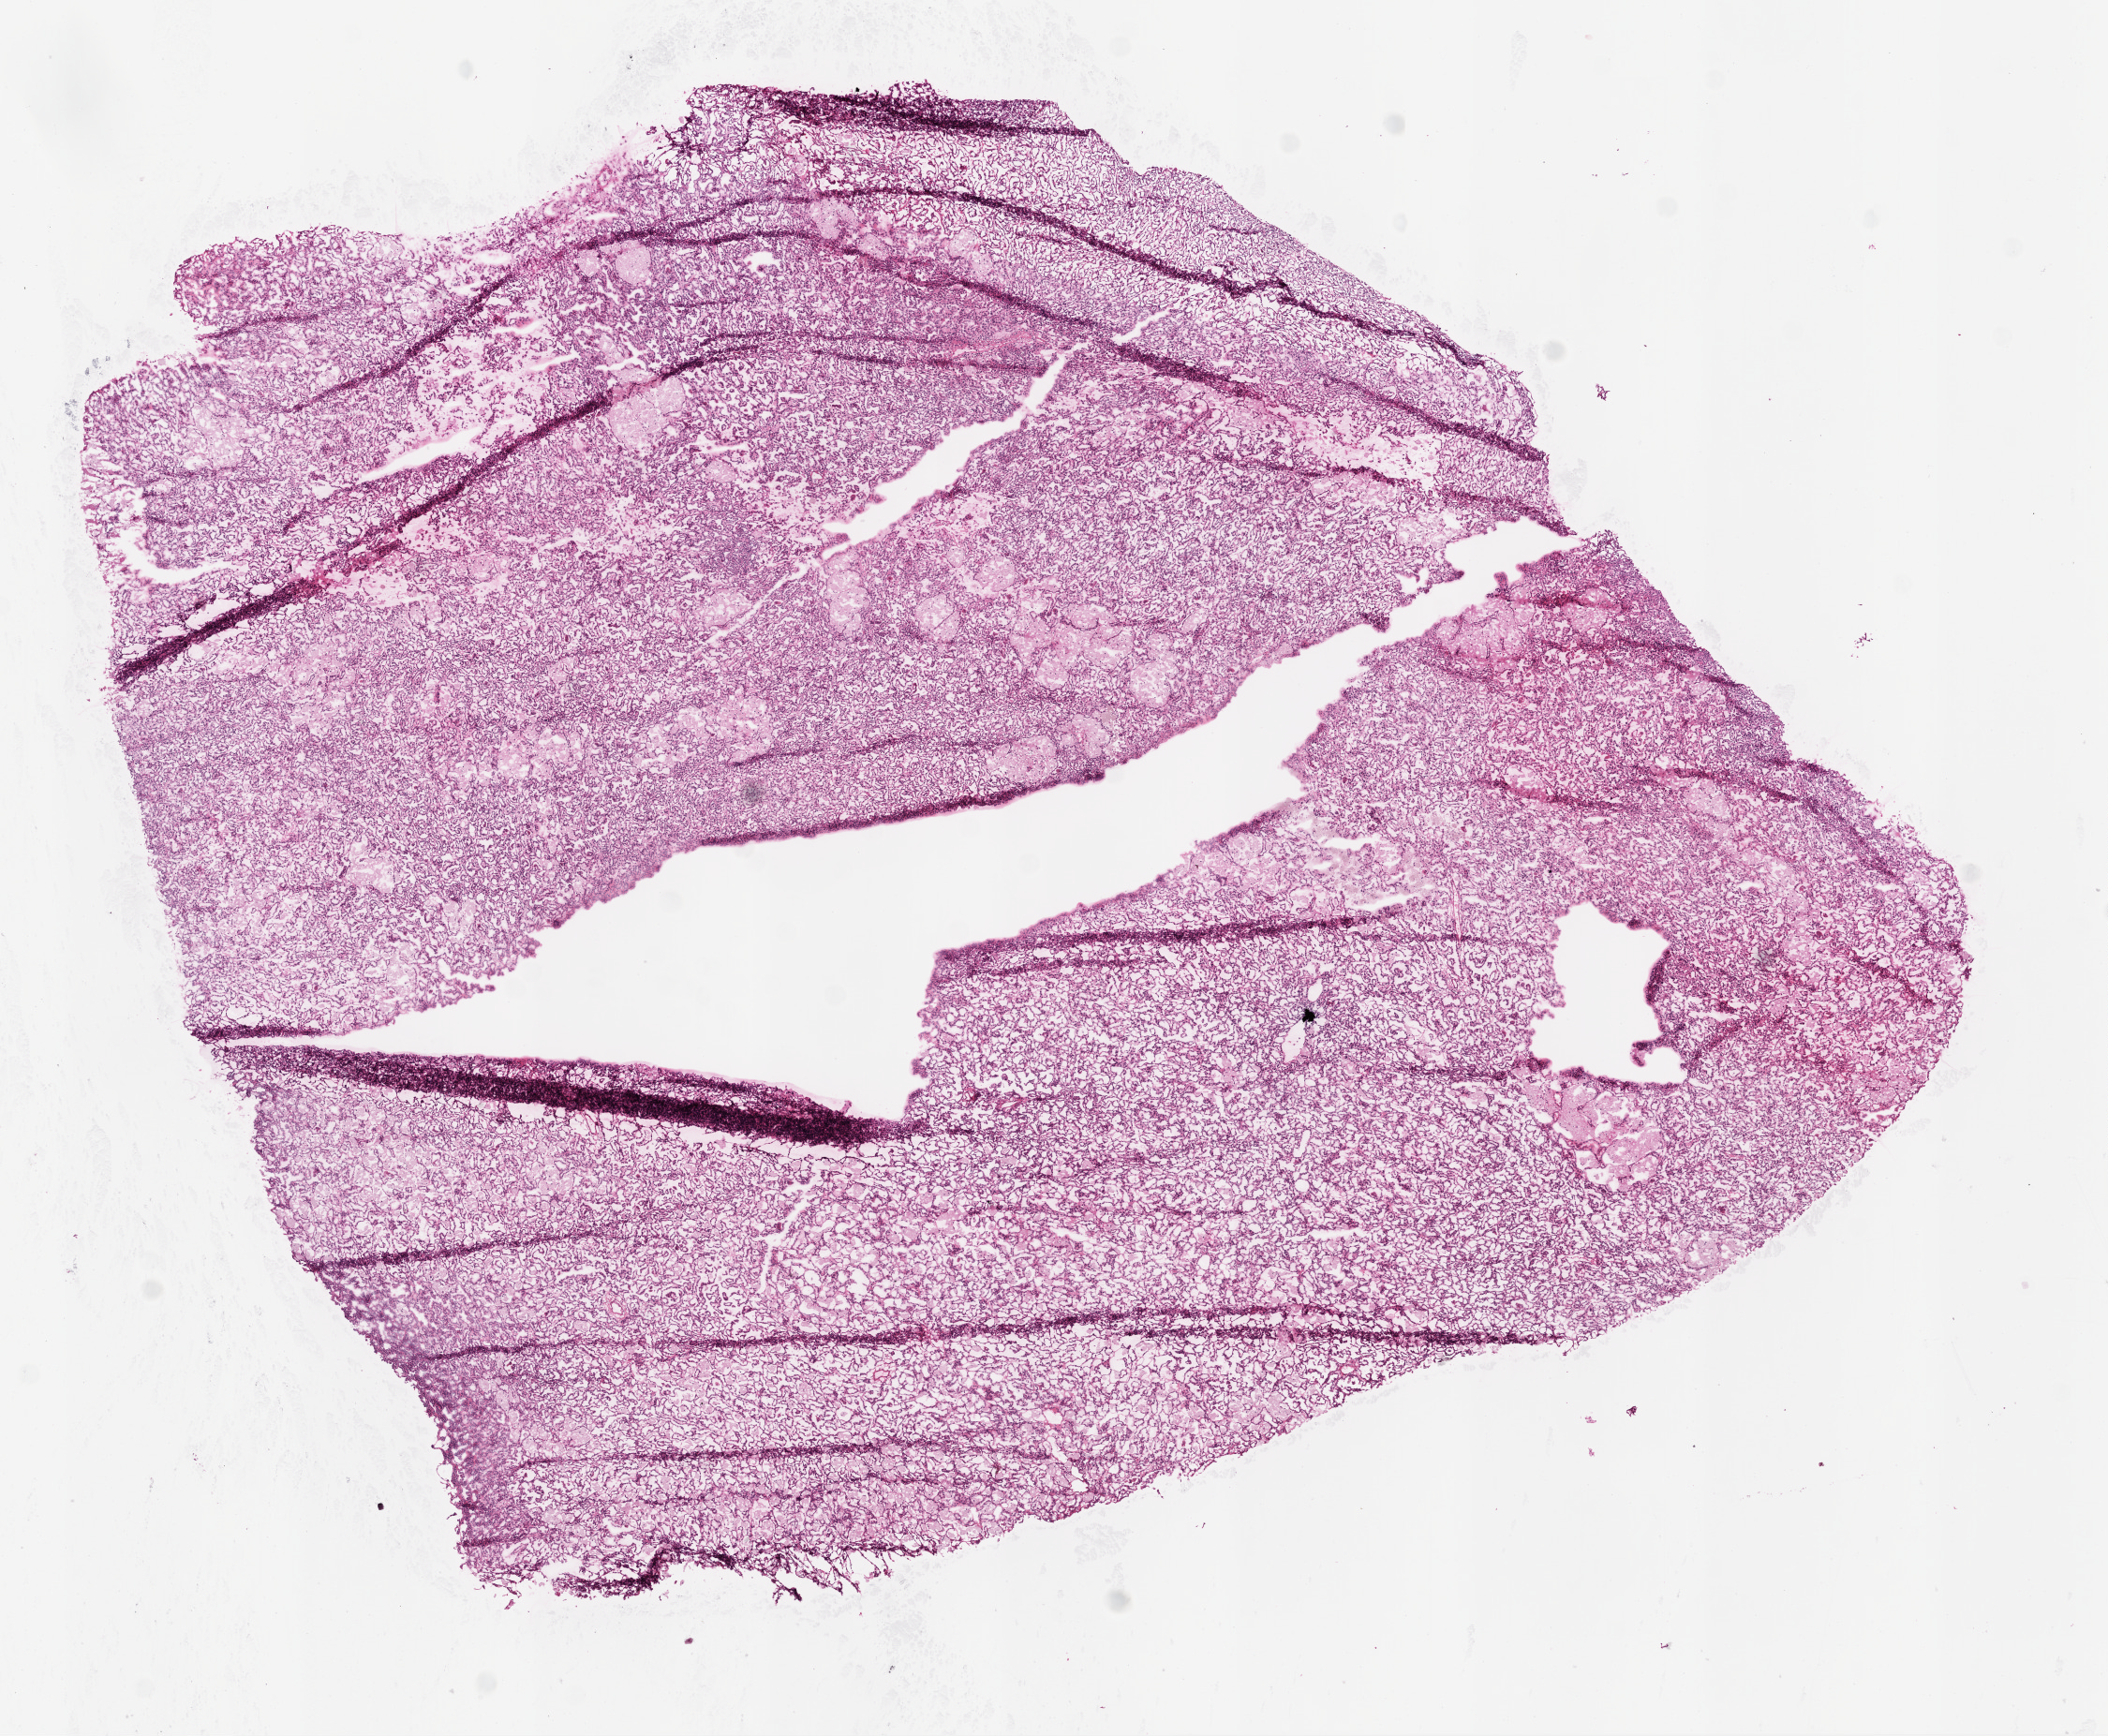
H&E whole-slide image — low-resolution overview of the scanned area, about 9.0 x 7.4 mm (from a 20x scan), frozen section from the top of the tissue portion, primary tumour sample from the kidney. Patient: male, age at initial diagnosis 57 years. Composition of this section per pathologist review: tumour cells 95%, tumour nuclei 80%, normal cells 0%, stromal cells 5%, necrosis 0%.
Pathologic diagnosis: Papillary adenocarcinoma, NOS. Laterality: left.